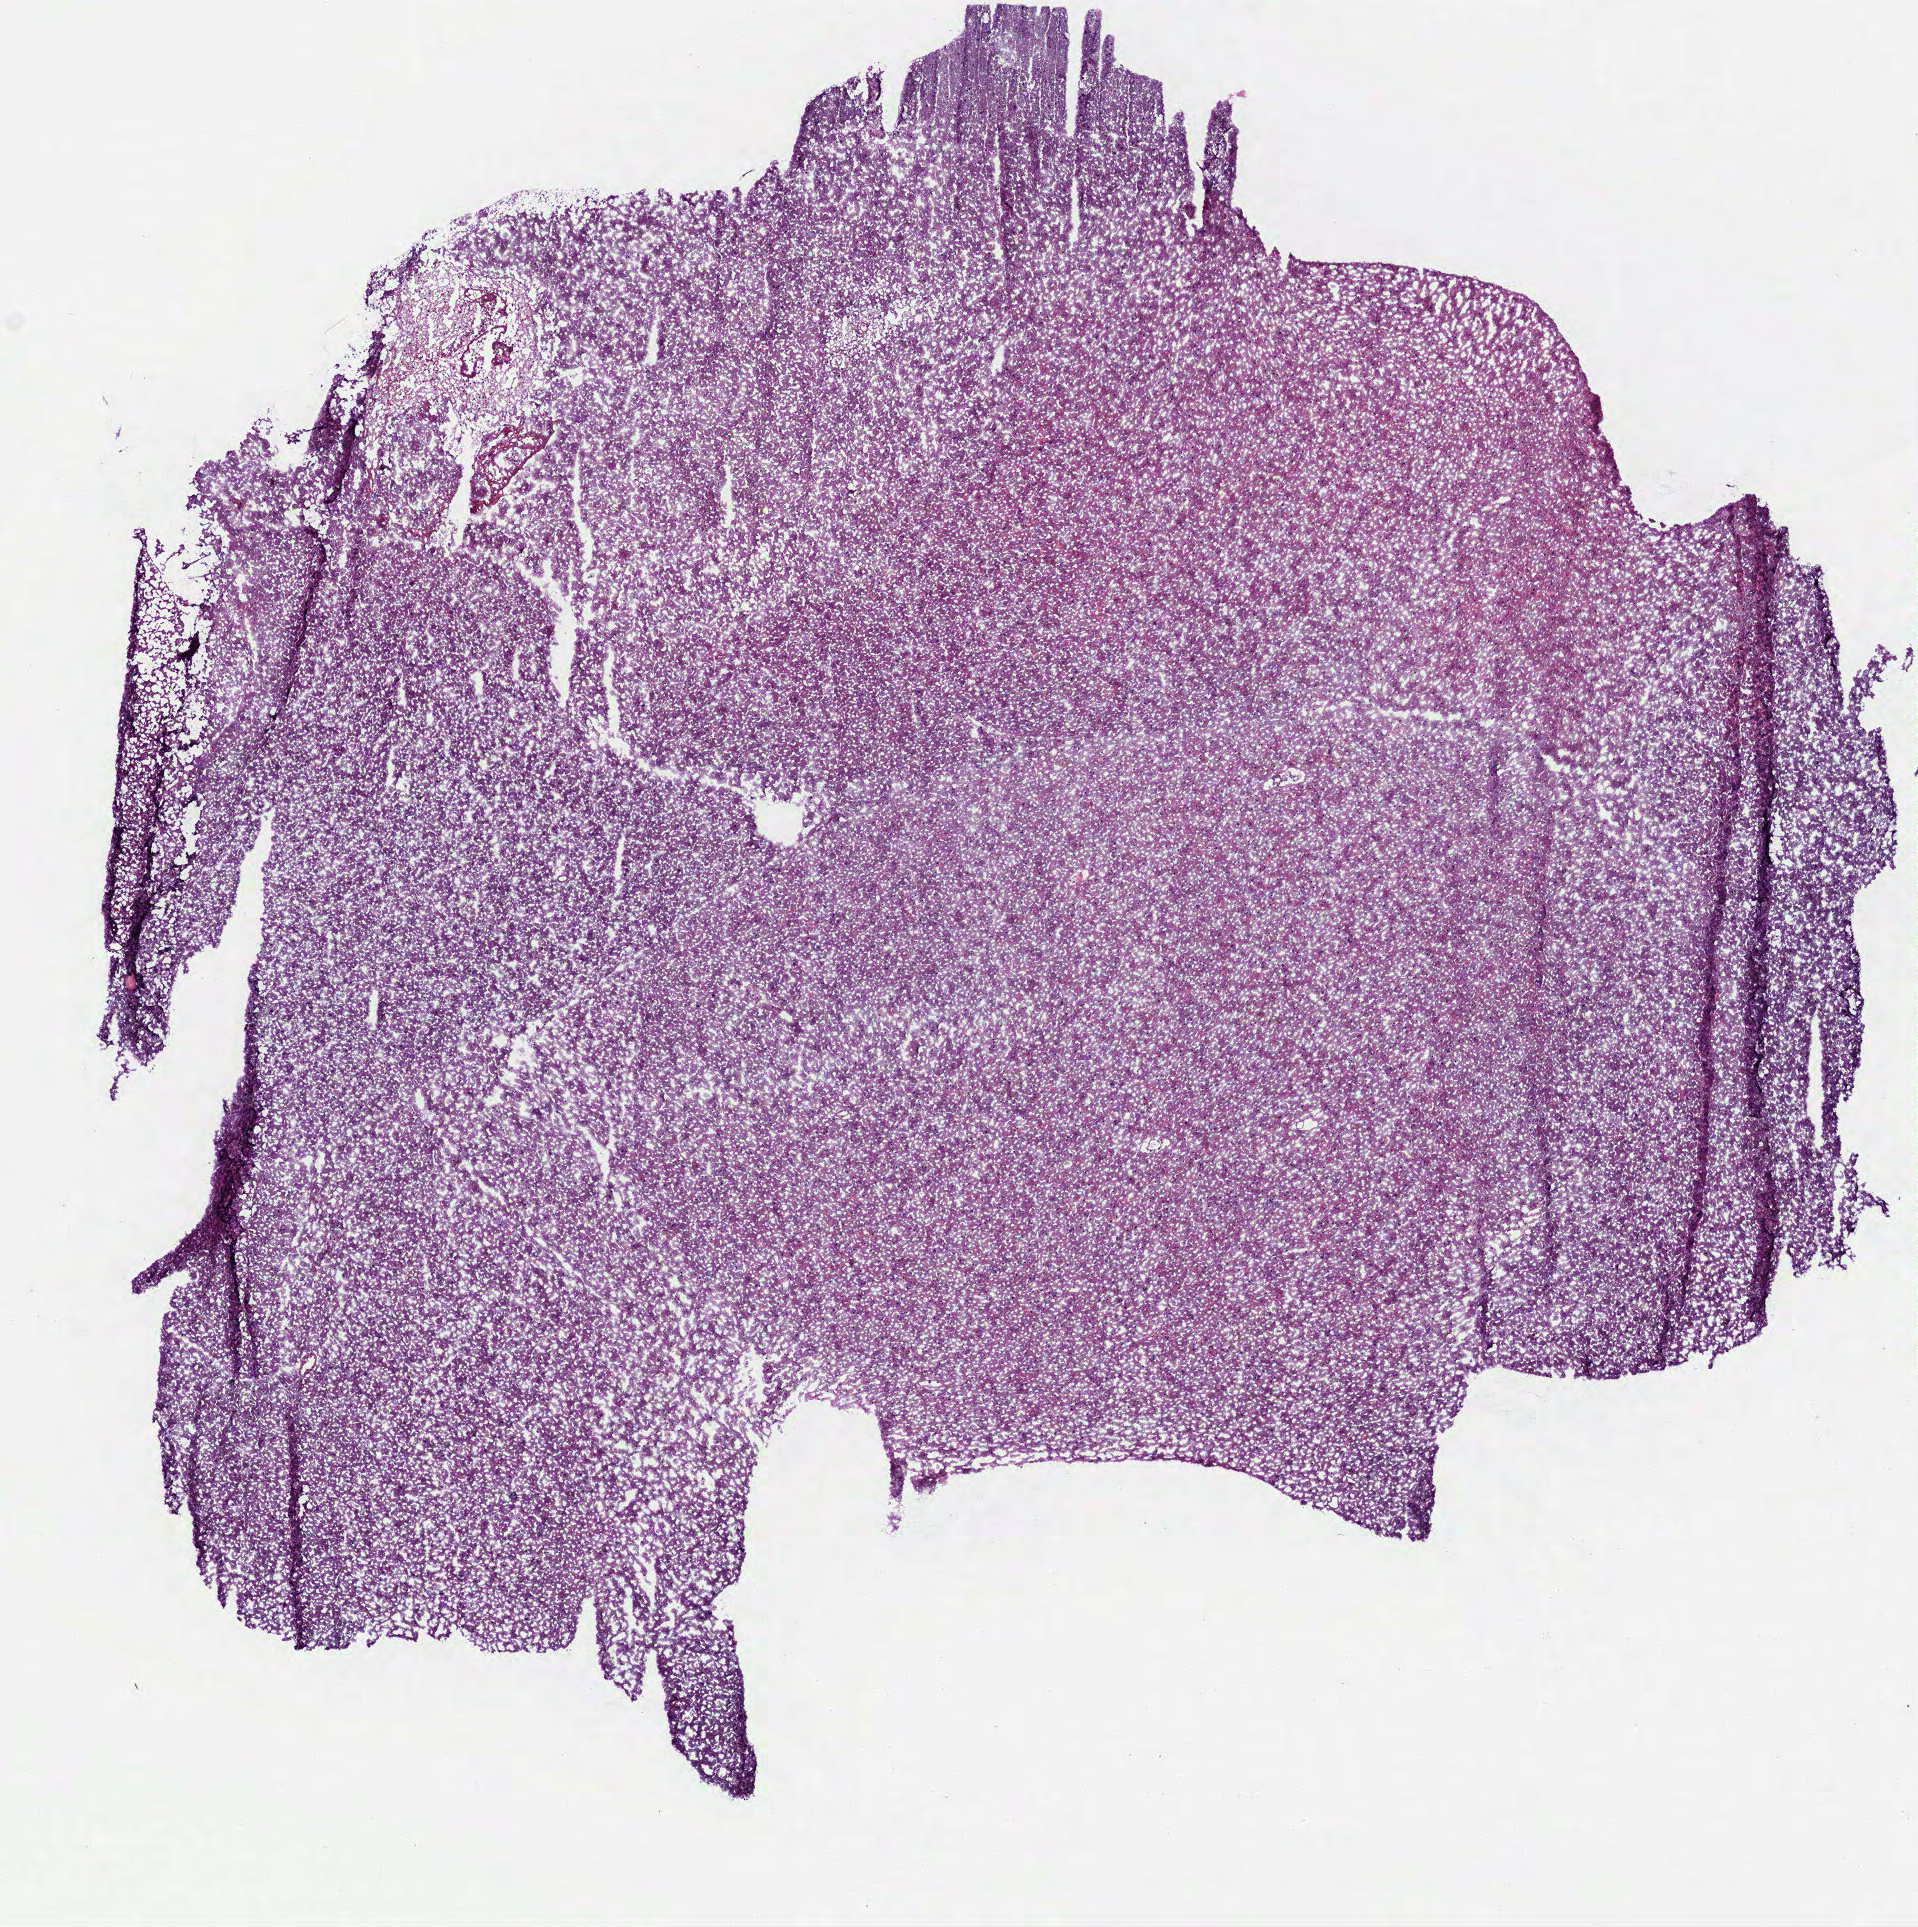
Hematoxylin and eosin (H&E) stained whole-slide image, whole scanned area (about 7.7 x 7.8 mm) shown as a low-resolution overview; frozen section from the top of the tissue portion; sample: primary tumour, brain. Male, age 30 years at initial diagnosis. Histologic grade: G2 (moderately differentiated). Slide review estimates, as recorded: tumour cells 100%, tumour nuclei 65%, normal cells 0%, stromal cells 0%, necrosis 0%.
Pathologic diagnosis: Mixed glioma (cerebrum).